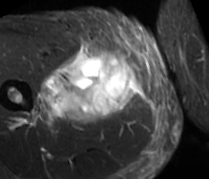
MRI of an extremity soft-tissue mass, one axial slice. Position 33 of 89 along the scan axis. STIR. MR volume resampled by the dataset authors to the PET/CT grid (not the native acquisition matrix). 209 × 179 image matrix. Male patient. Case-level facts recorded for this patient, not image findings: histological type: undifferentiated - pleiomorphic; grade: high; site of the primary tumour: right thigh.
Annotated regions visible in this slice (expert contour drawn on MRI and transferred to this co-registered scan by the dataset authors):
- gross tumour volume including surrounding oedema: bounding box [x1, y1, x2, y2] px = [32, 46, 138, 124]
- gross tumour volume (mass): [62, 53, 138, 122]